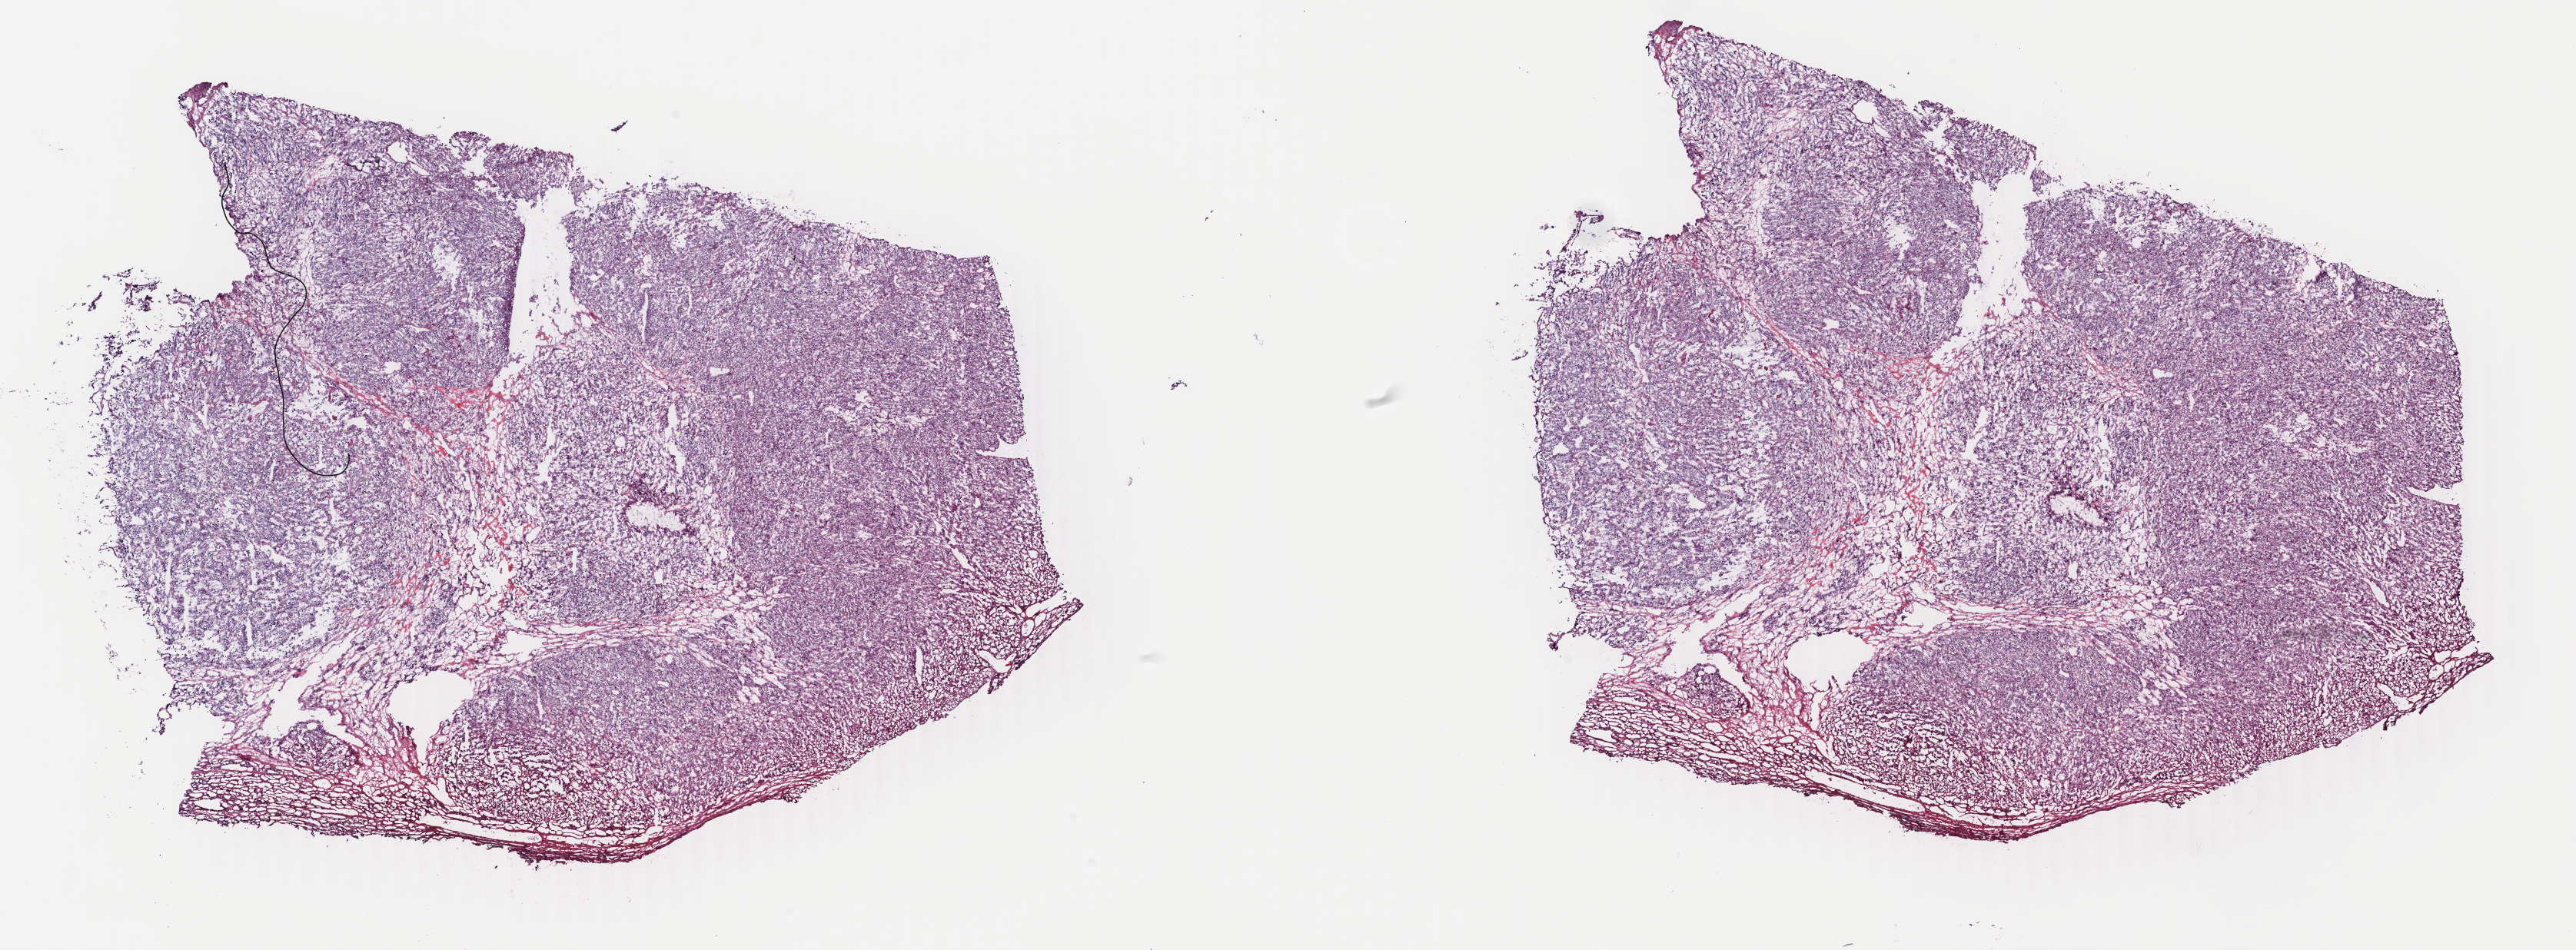
Whole-slide histology image, H&E, low-resolution overview of the scanned area, about 26.7 x 9.8 mm (slide scanned at 40x). Frozen section from the top of the tissue portion. Sample: primary tumour, adrenal gland. Patient: female, age at initial diagnosis 19 years. Slide review estimates, as recorded: tumour cells 100%, tumour nuclei 80%, normal cells 0%, stromal cells 0%, necrosis 0%. Infiltration values recorded for this section: lymphocyte infiltration 2%, monocyte infiltration 0%, neutrophil infiltration 0%.
Diagnosis: Pheochromocytoma, NOS.